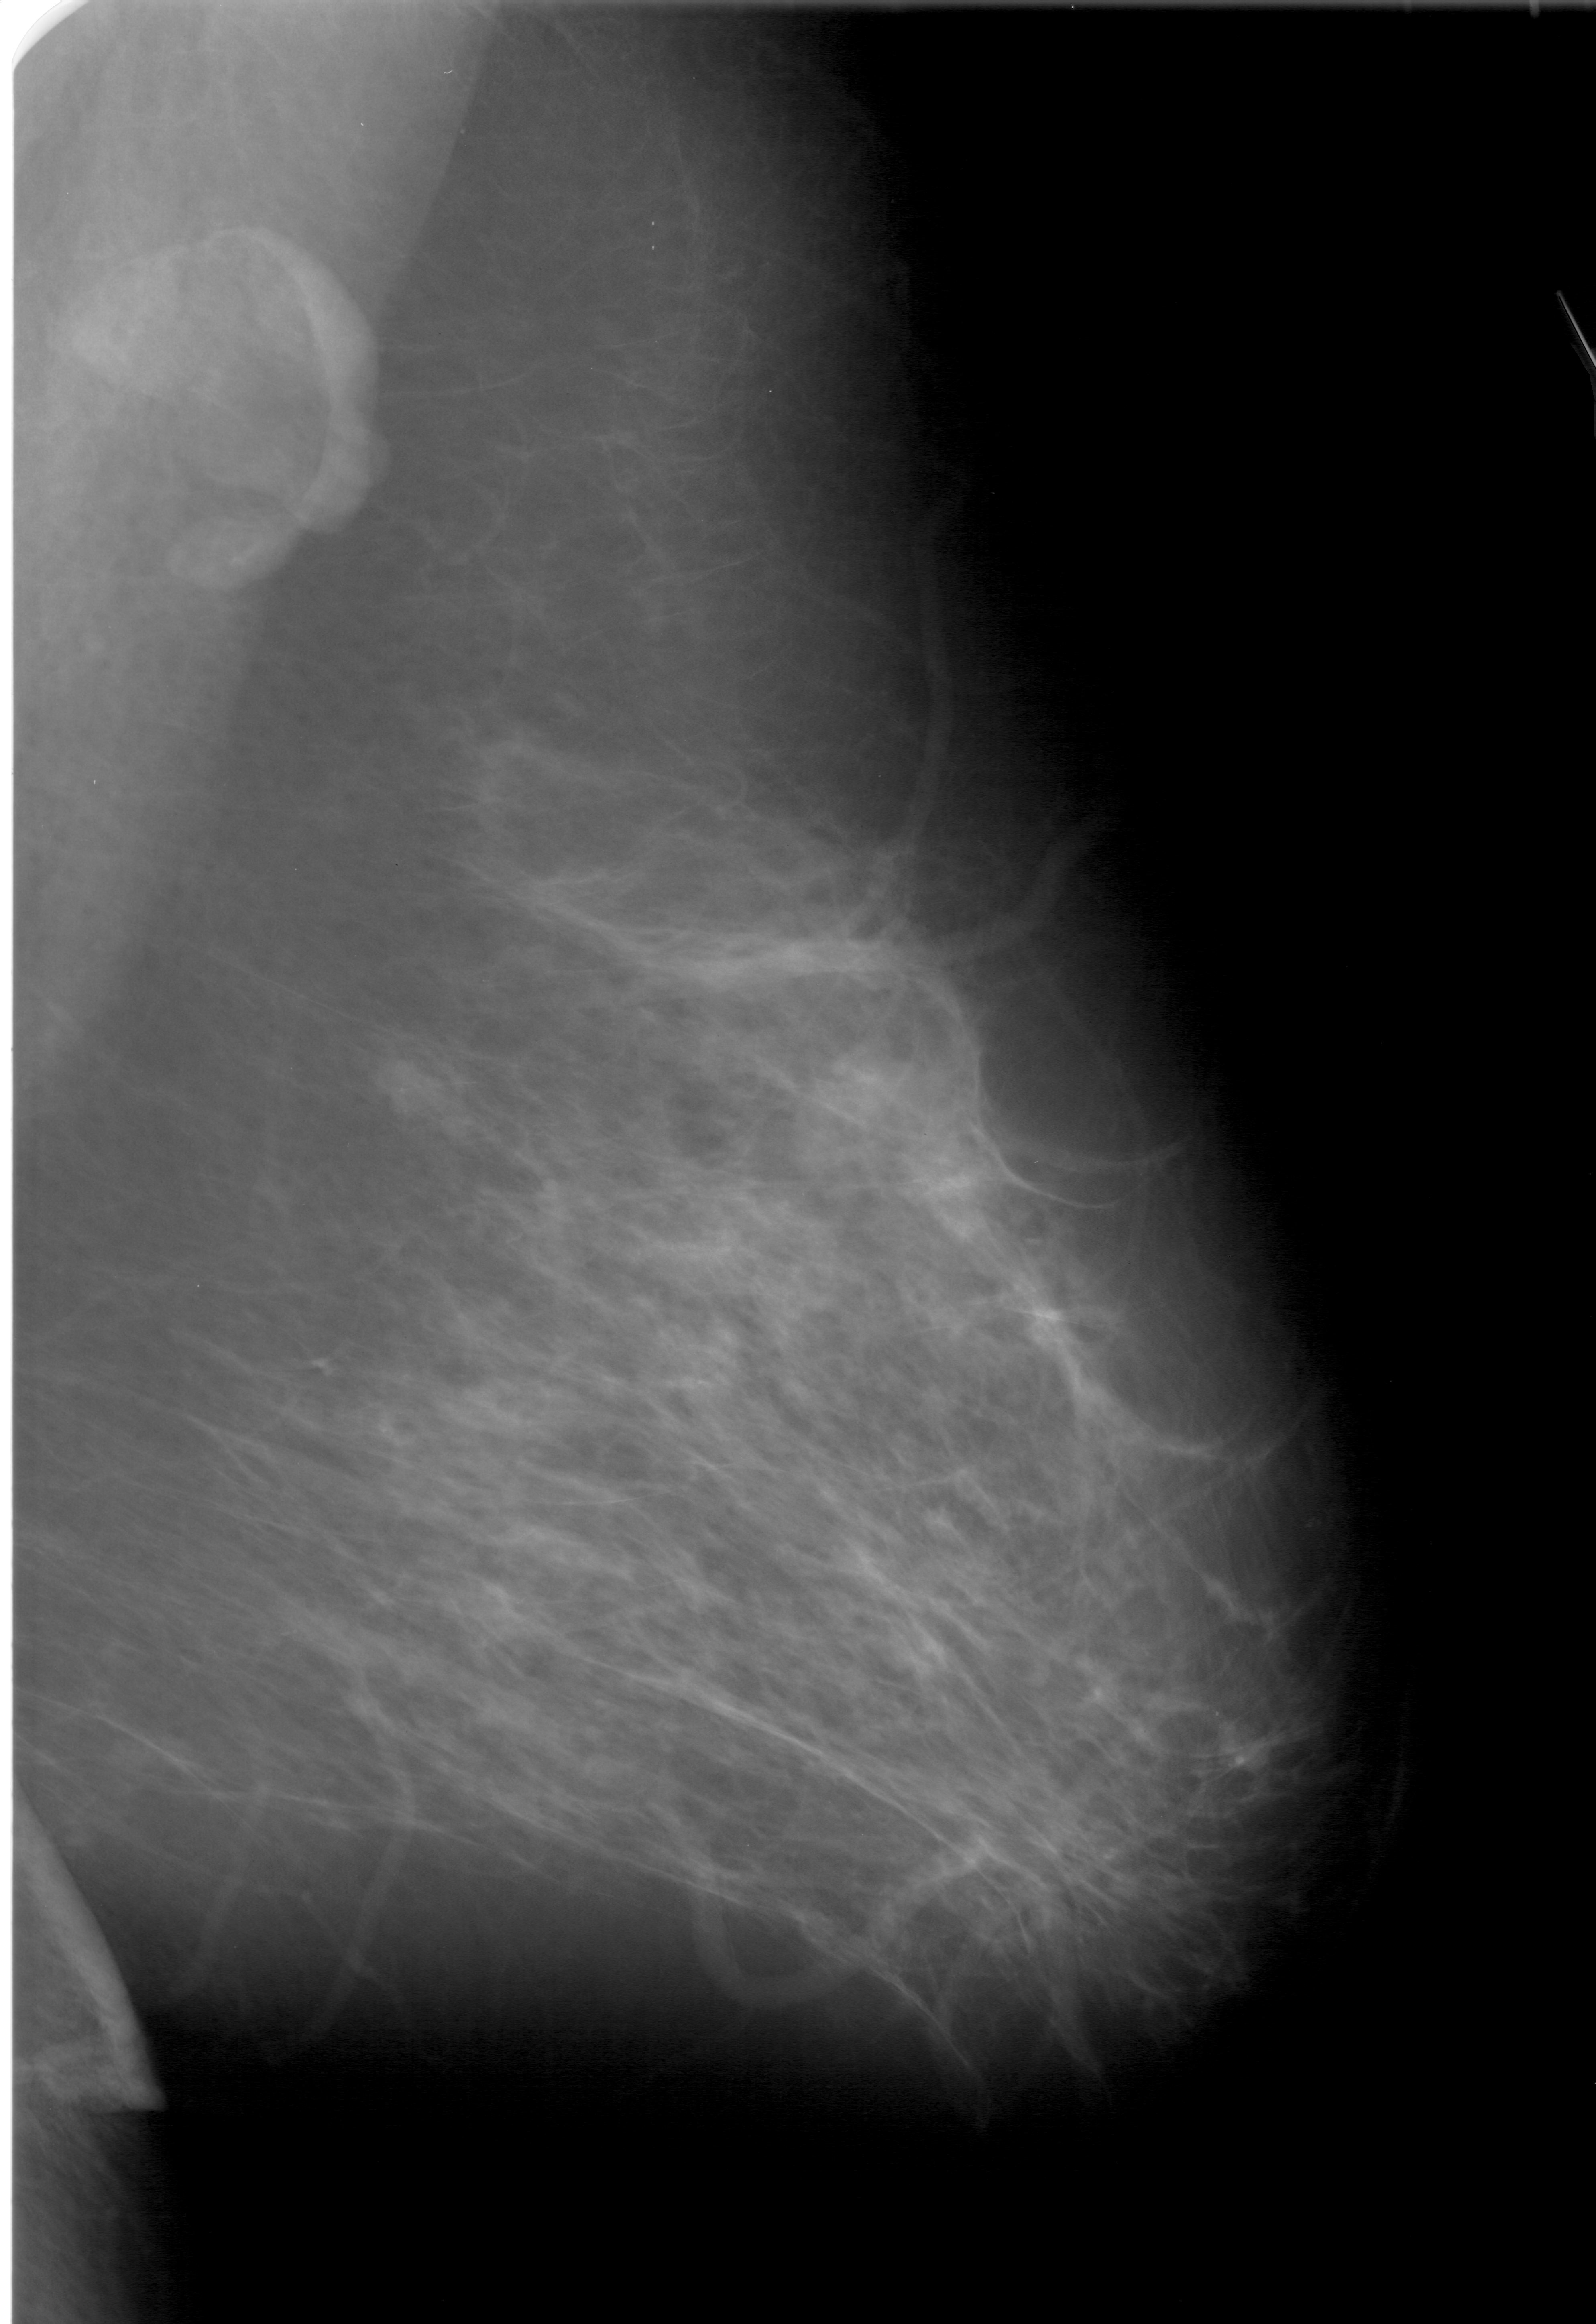
Digitized screen-film mammogram. Right breast. Mediolateral oblique (MLO) view. BI-RADS breast density category 3 (scale 1–4). 1596 × 2324 image matrix.
Expert-marked regions of interest on this image (one box per marked abnormality):
- mass, shape lobulated, margins ill defined; BI-RADS assessment category 4; subtlety rating 4 on a 1 (subtle) to 5 (obvious) scale; pathology (as recorded): malignant: bounding box [x1, y1, x2, y2] px = [351, 1024, 462, 1132]